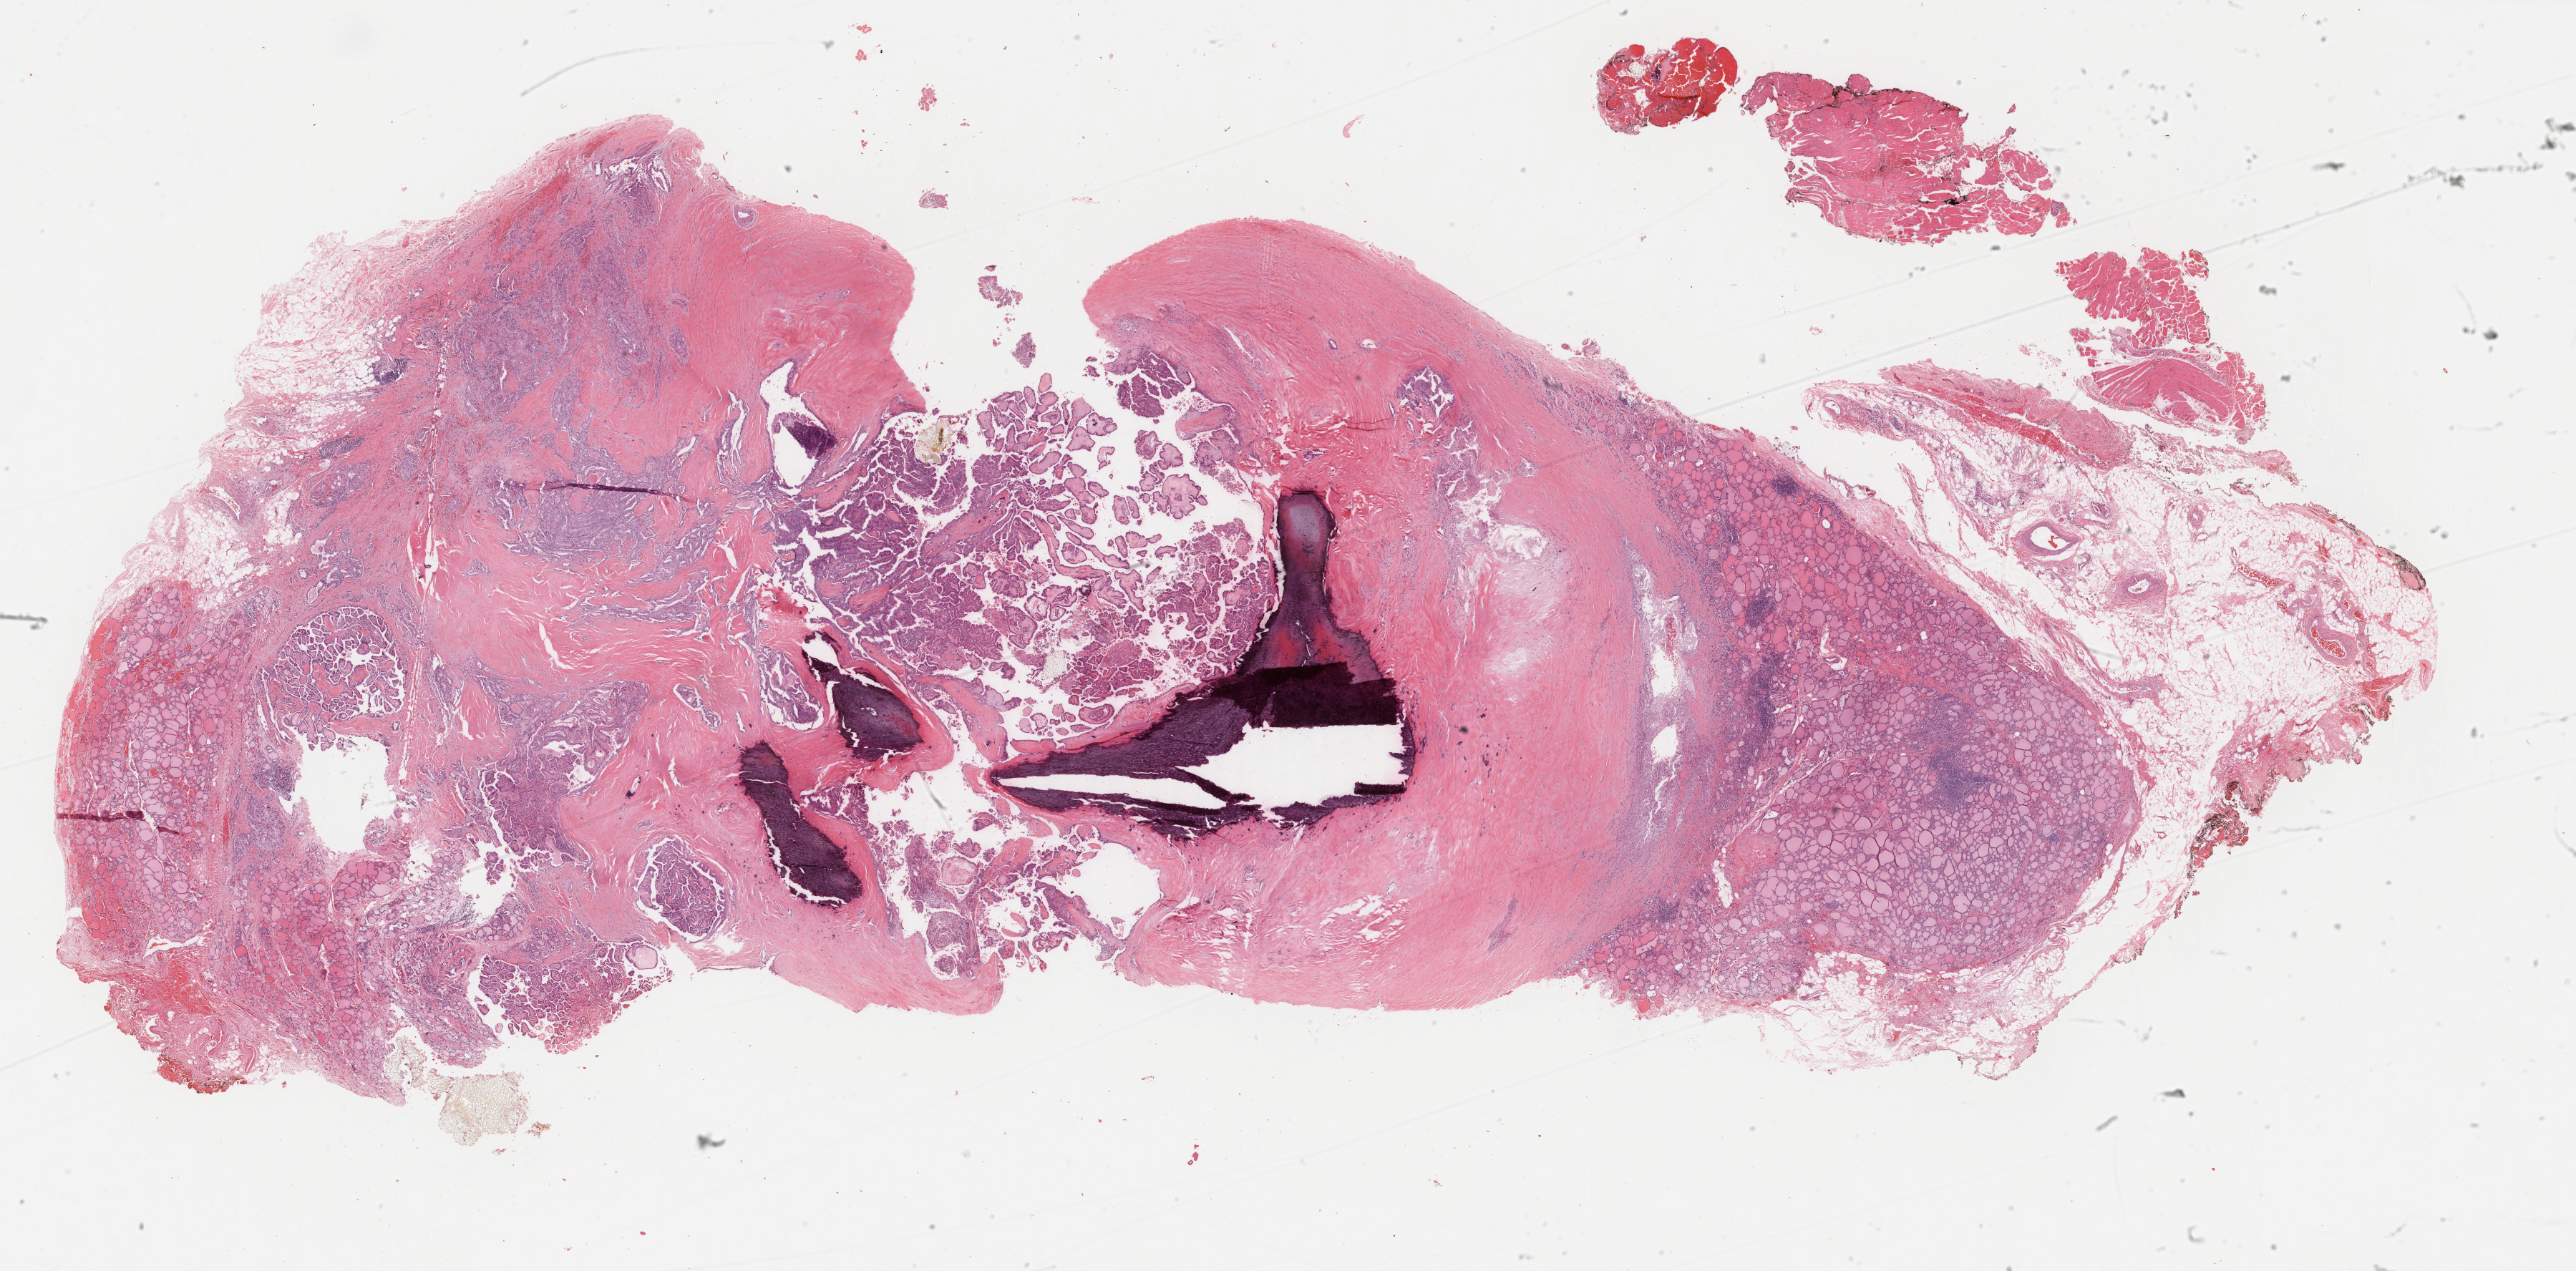
H&E whole-slide image, low-resolution overview of the scanned area, about 28.6 x 14.1 mm. Formalin-fixed paraffin-embedded (FFPE) diagnostic section. Primary tumour sample from the thyroid. Patient: female, age at initial diagnosis 41 years.
AJCC pathologic stage: I. TNM: T2 N1 M0. Lymph nodes positive (case pathology): 3 of 40 examined. Pathologic diagnosis: Papillary adenocarcinoma, NOS (thyroid gland).